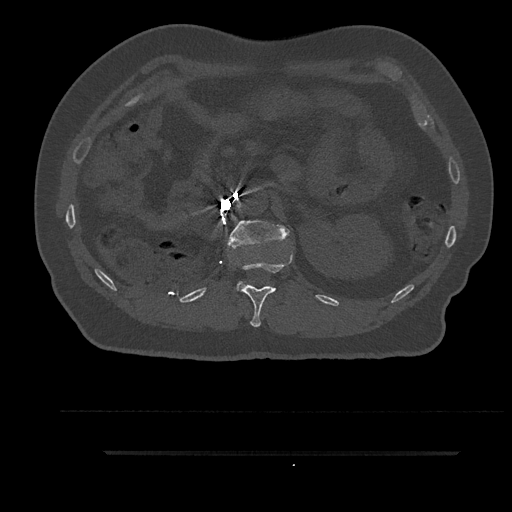
CT including the spine, one axial slice; position 215 of 797 along the scan axis; bone window (W 1800 / L 400 HU); 512 × 512 image matrix, field of view 432 × 432 mm. Patient: male, 63 years. From the clinical record (not read from this slice): primary cancer: renal; vertebrae with lytic lesions (as recorded): T8.
Annotated regions visible in this slice (semi-automatic segmentation, software-assisted and operator-edited):
- L1 vertebra: bounding box [x1, y1, x2, y2] px = [227, 220, 290, 290]
- T12 vertebra: [240, 252, 293, 327]